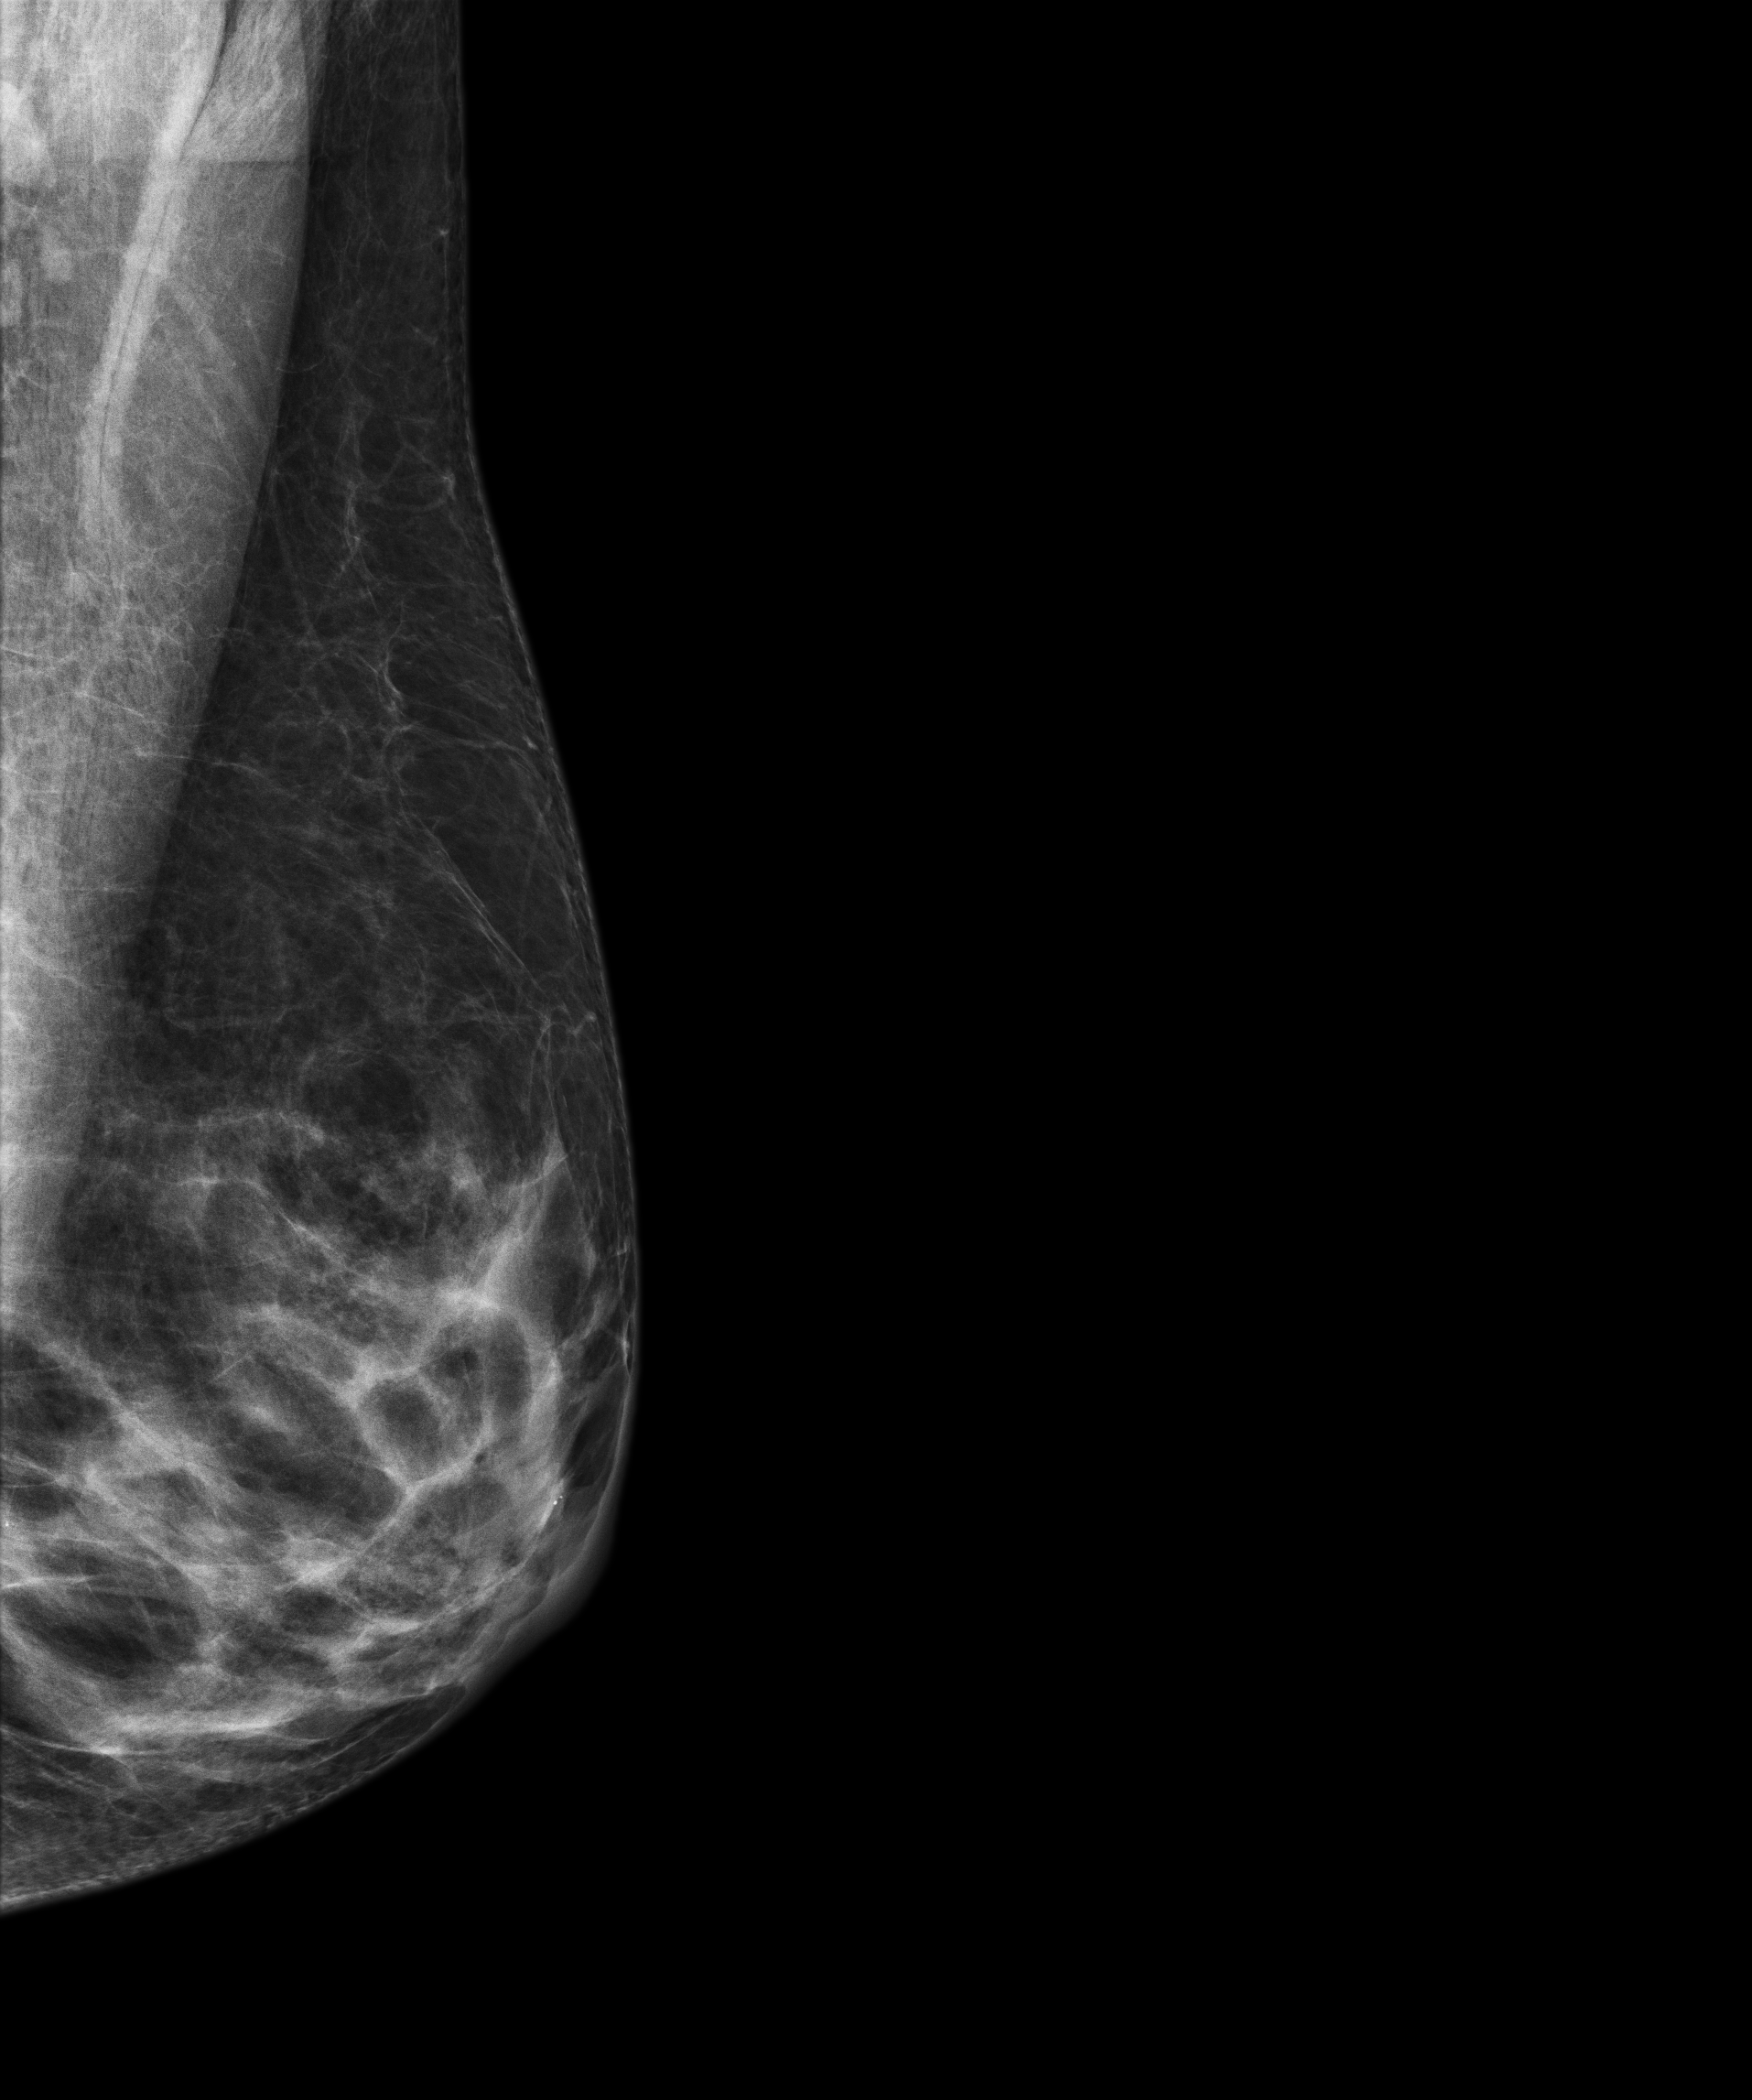
Annual screening mammography examination, compressed breast thickness 49 mm. Patient: female, 67 years.
Image type: full-field digital mammogram. Breast: left. Projection: MLO view.